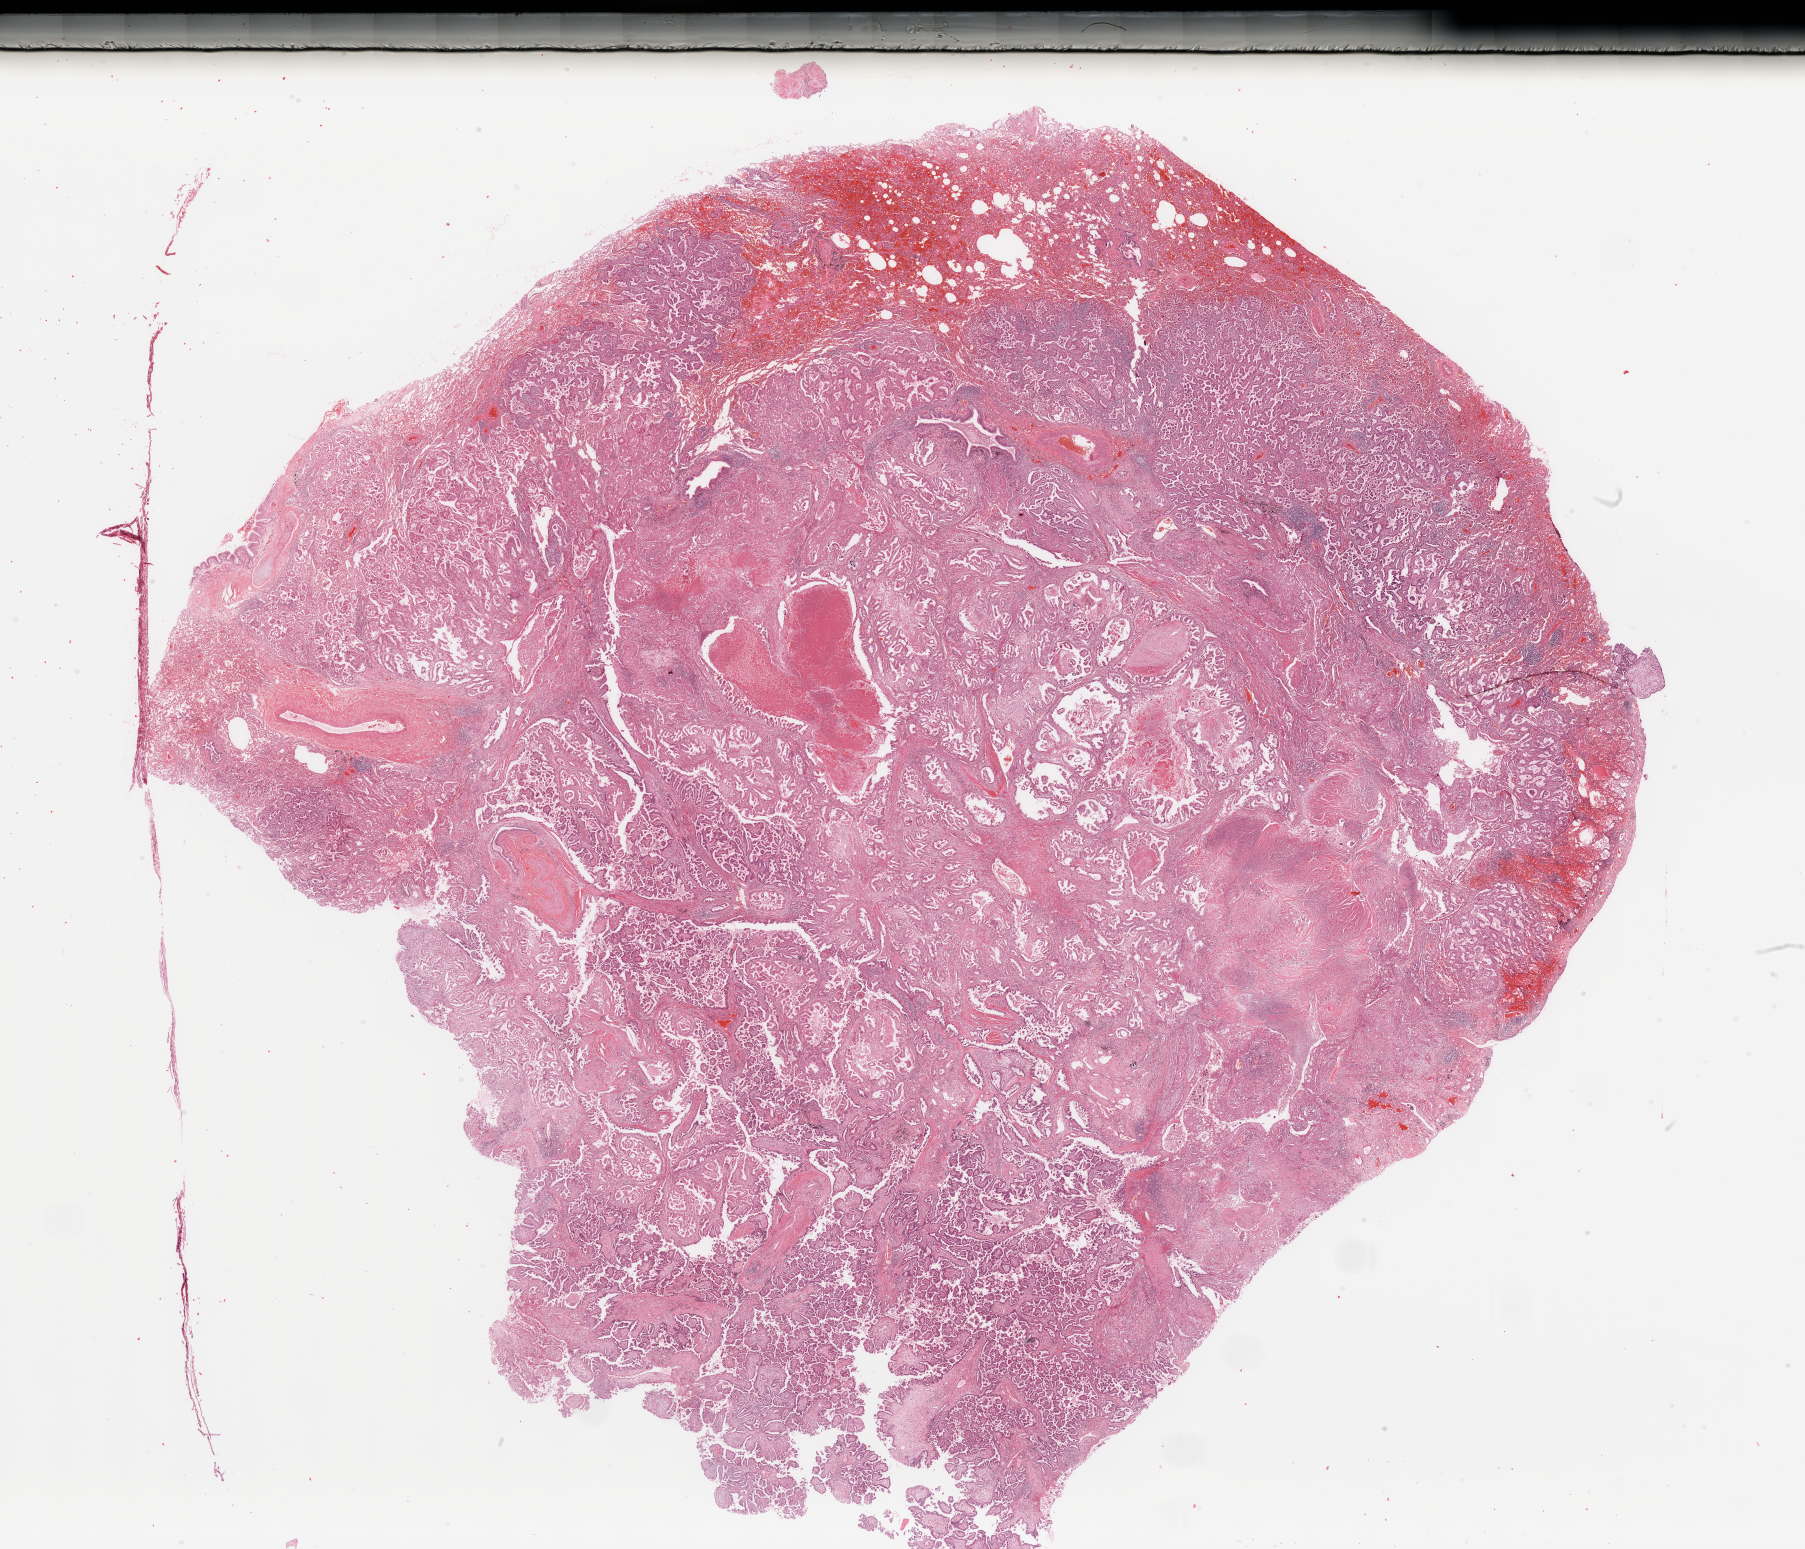
Digitized H&E-stained tissue section (whole slide) — a low-resolution overview of the entire scanned area, about 28.5 x 24.5 mm (acquisition: 20x scan). Lung, tumour tissue. Female, 60 y/o. Histologic grade: G2 (moderately differentiated).
• AJCC pathologic stage: IB
• diagnosis: Adenocarcinoma, NOS